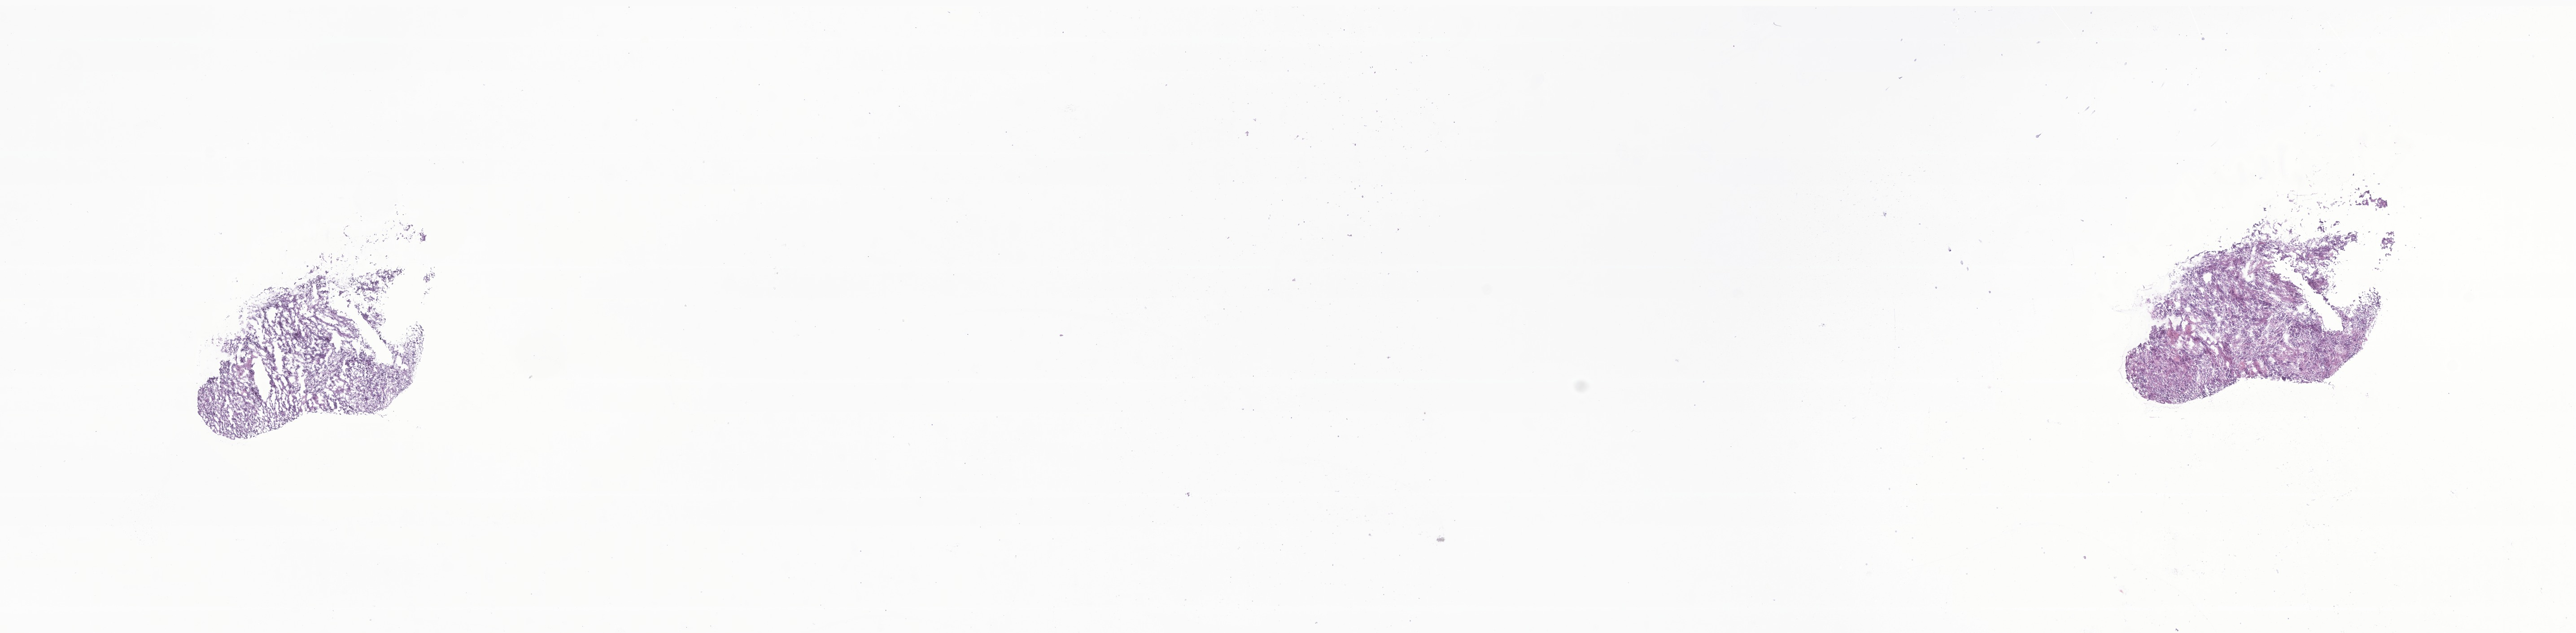
Digitized H&E-stained section of tumor tissue from the abdomen, whole scanned area (about 24.2 x 5.9 mm) shown as a low-resolution overview. Frozen section (OCT-embedded). Patient: female, age 639 days (about 1.7 years).
Recorded diagnosis: Neuroblastoma, NOS.